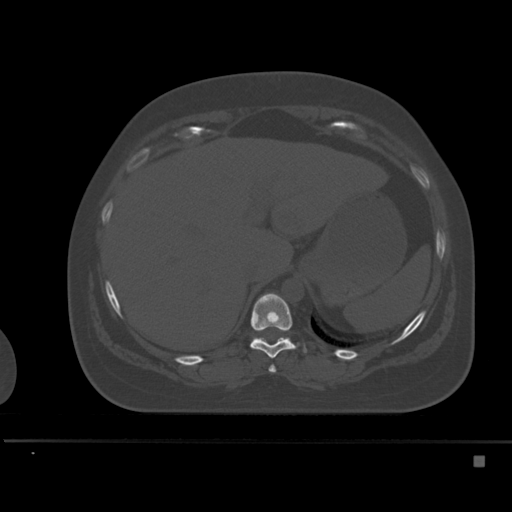
CT including the spine, one axial slice; position 246 of 495 along the scan axis; bone window (W 1800 / L 400 HU); 1.5 mm slice thickness; 512 × 512 image matrix. Female patient, age 33 years. From the clinical record (not read from this slice): primary cancer: breast; vertebrae with lytic lesions (as recorded): T1.
Structures marked on this image (semi-automatic segmentation, software-assisted and operator-edited):
- T10 vertebra: bounding box [x1, y1, x2, y2] px = [249, 293, 306, 358]
- T9 vertebra: [269, 365, 277, 373]